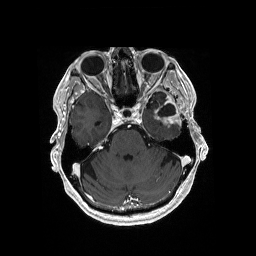
Brain MRI from a brain-tumour surgery series, one axial slice. Slice 125 of 176 in the series (ordered by position). T1-weighted post-contrast. 256 × 256 image matrix, field of view 256 × 256 mm. Case-level facts recorded for this patient, not image findings: histopathology: Glioblastoma; WHO grade: 4; IDH mutation: no; tumour location: Left Medial Temporal.
Structures marked on this image (expert manual segmentation):
- previous resection cavity: bounding box [x1, y1, x2, y2] px = [158, 103, 175, 117]
- tumour: [154, 114, 181, 129]